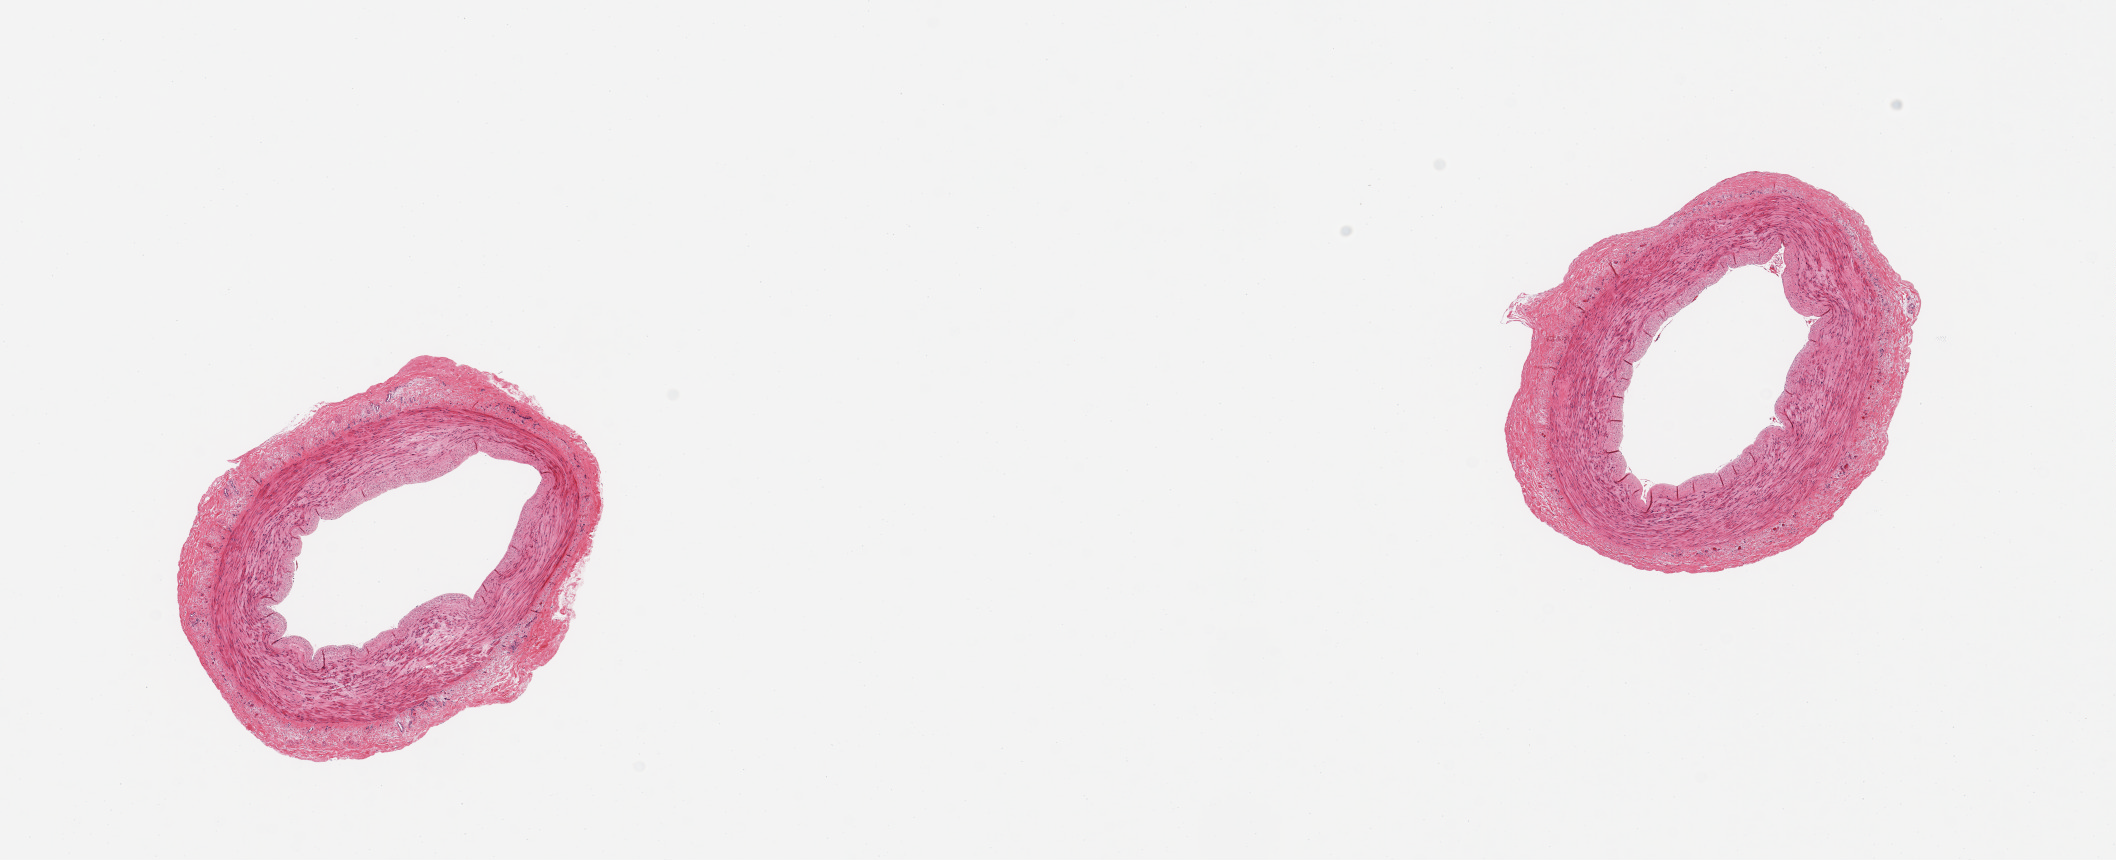
Whole-slide image, H&E stain — a low-resolution overview of the entire scanned area, about 16.7 x 6.8 mm; PAXgene-fixed, paraffin-embedded tissue; sampled site (target tissue): tibial artery; tissue donor sample. Male donor.
Pathologist's review note for this sample: 2 pieces; no plaques; well dissected.